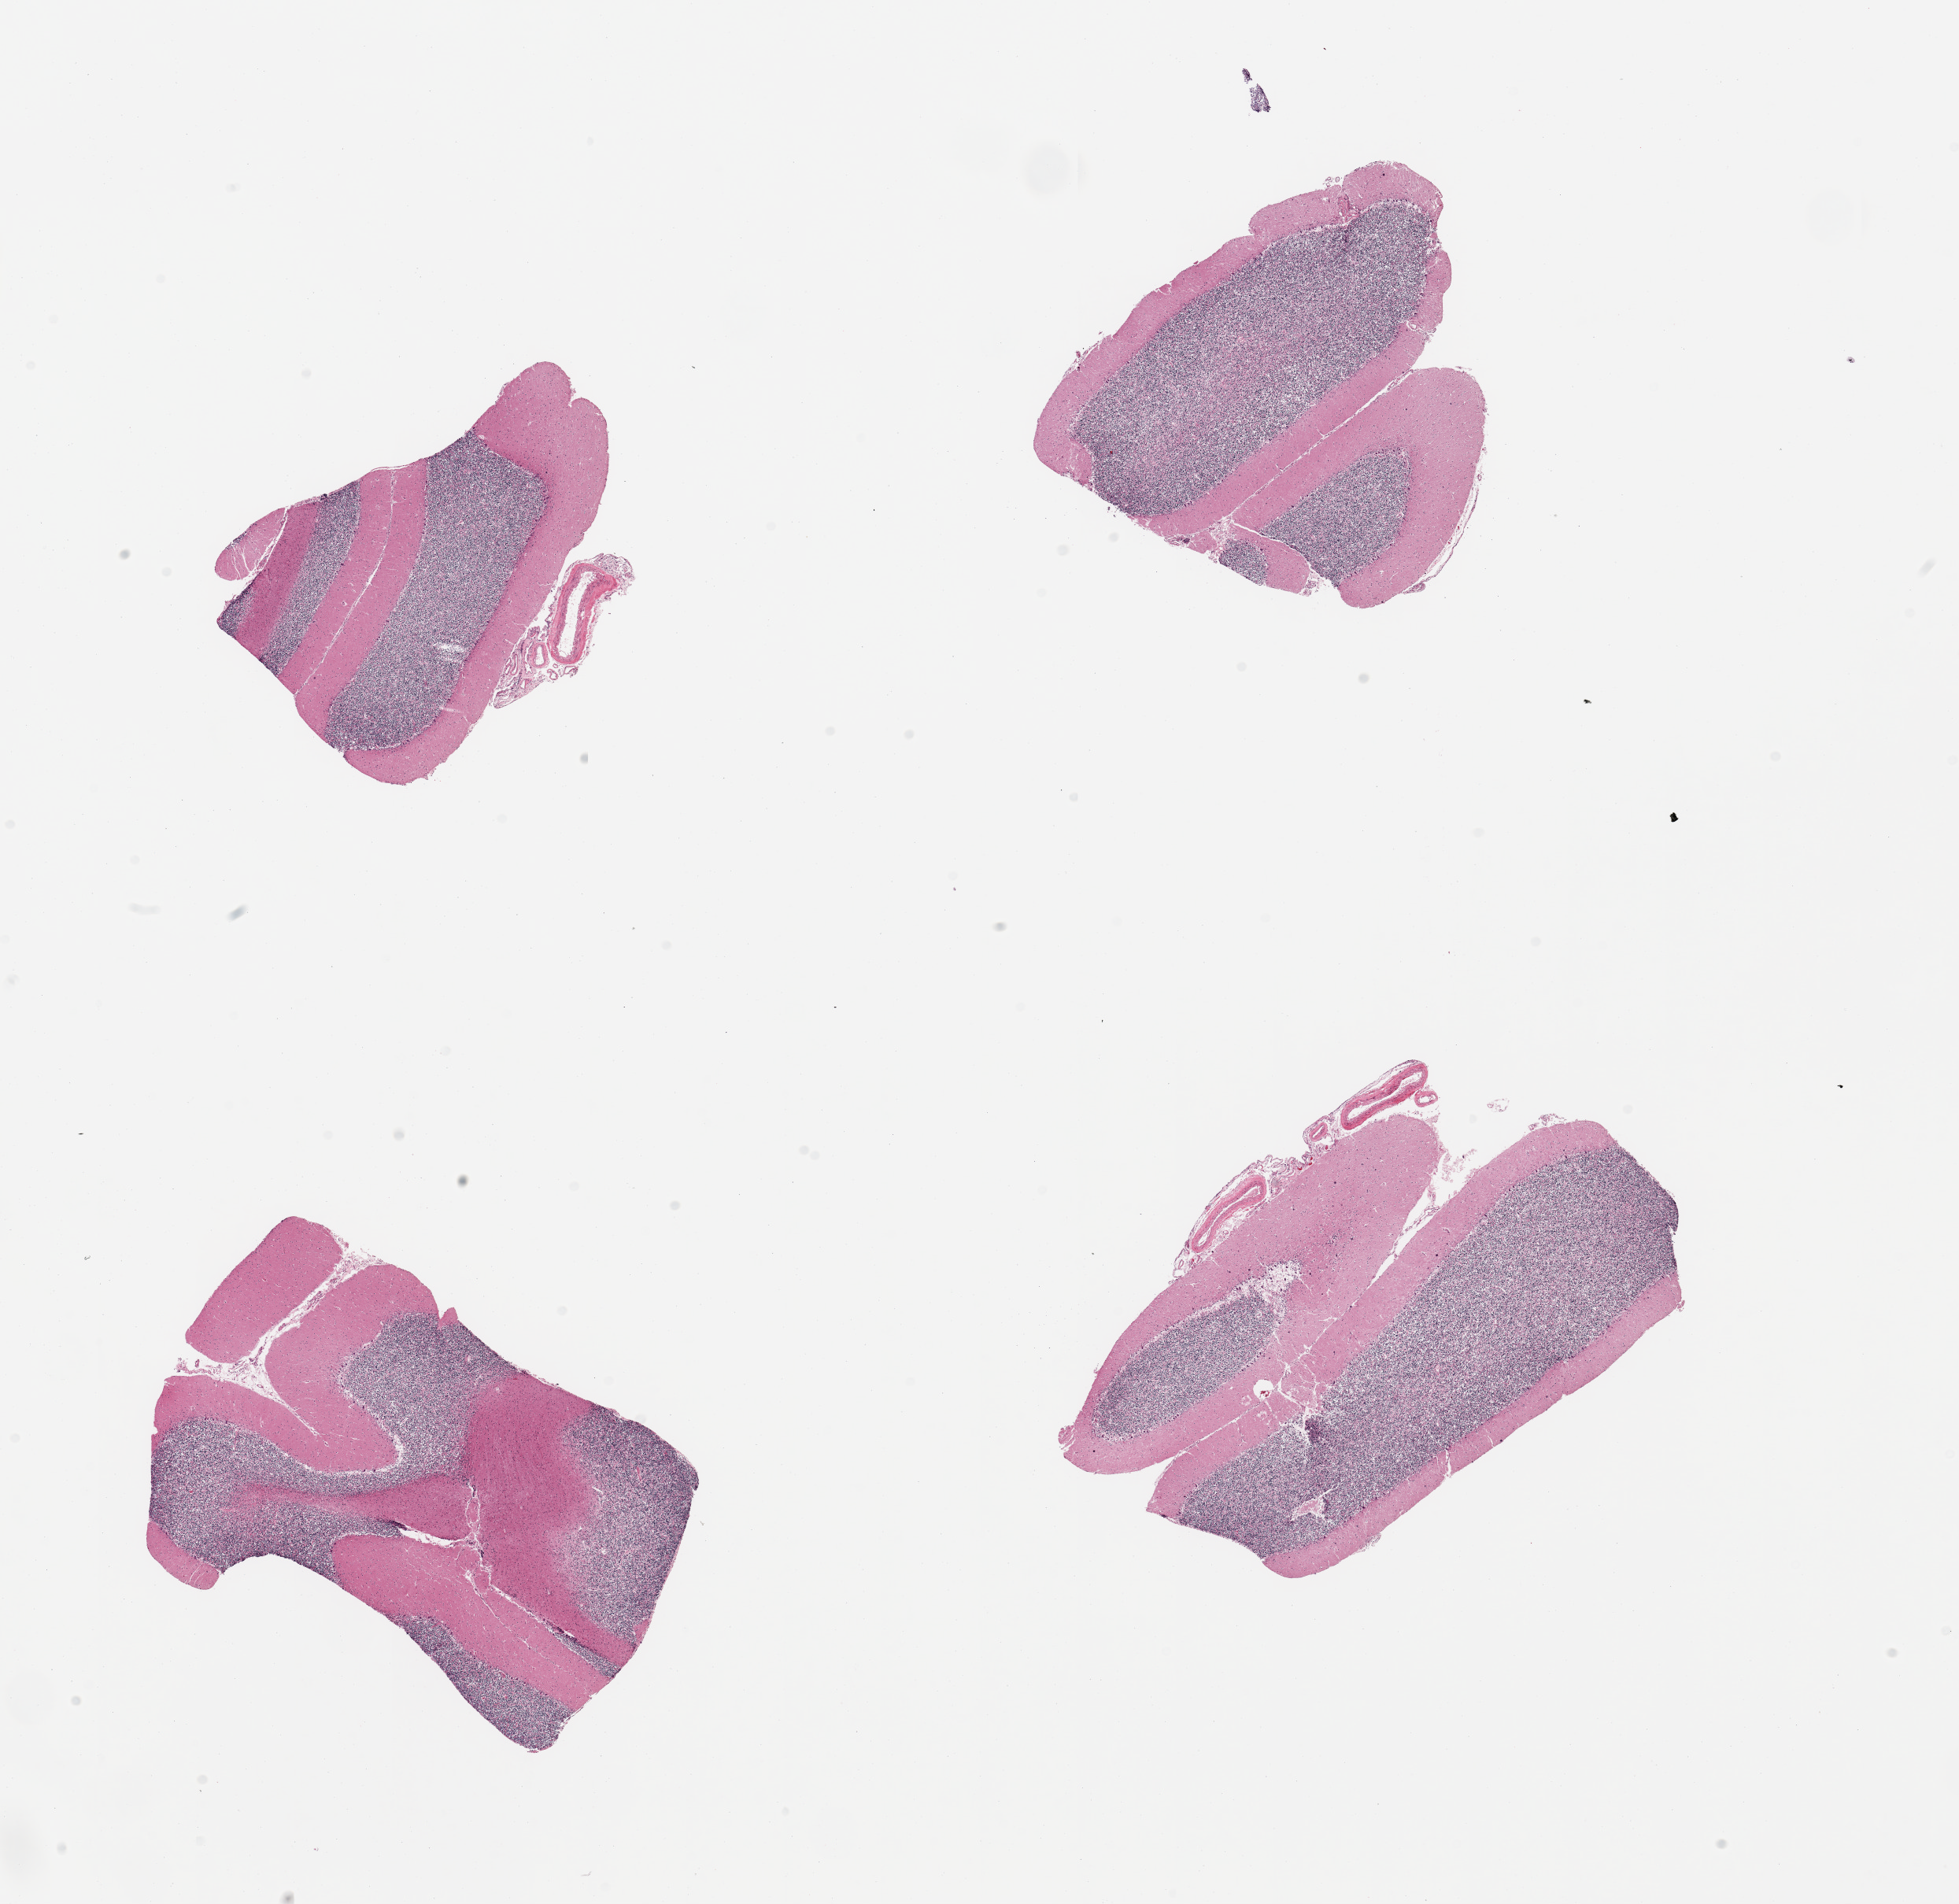
H&E whole-slide image, brightfield, whole scanned area (about 19.7 x 19.1 mm) shown as a low-resolution overview; PAXgene-fixed paraffin-embedded (PFPE) section; target tissue: cerebellum; donor tissue sample. Donor sex: female.
* pathologist's review note for this sample: 4 pieces, no abnormalities